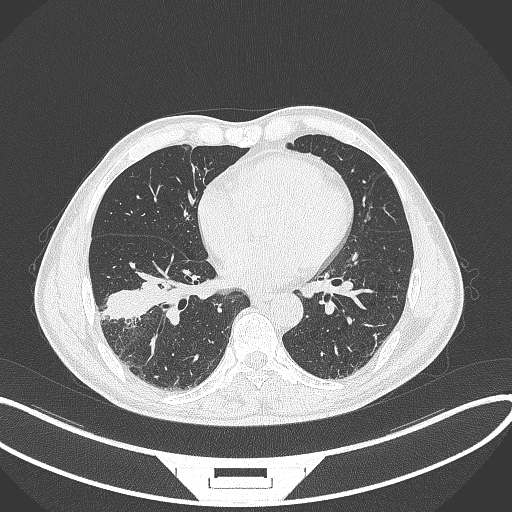
Chest CT, one axial slice. Slice 146 of 364 in the series (ordered by position). Reconstruction kernel B70f. Lung window (W 1500 / L -600 HU). 1 mm slice thickness. 512 × 512 image matrix. Male patient, age 58 years. Case-level facts recorded for this patient, not image findings: clinical TNM (as recorded): T3 N0 M0.
Outlined on this slice (bounding box drawn by a radiologist):
- lung tumour (recorded histology: squamous cell carcinoma): bounding box [x1, y1, x2, y2] px = [105, 271, 163, 328]